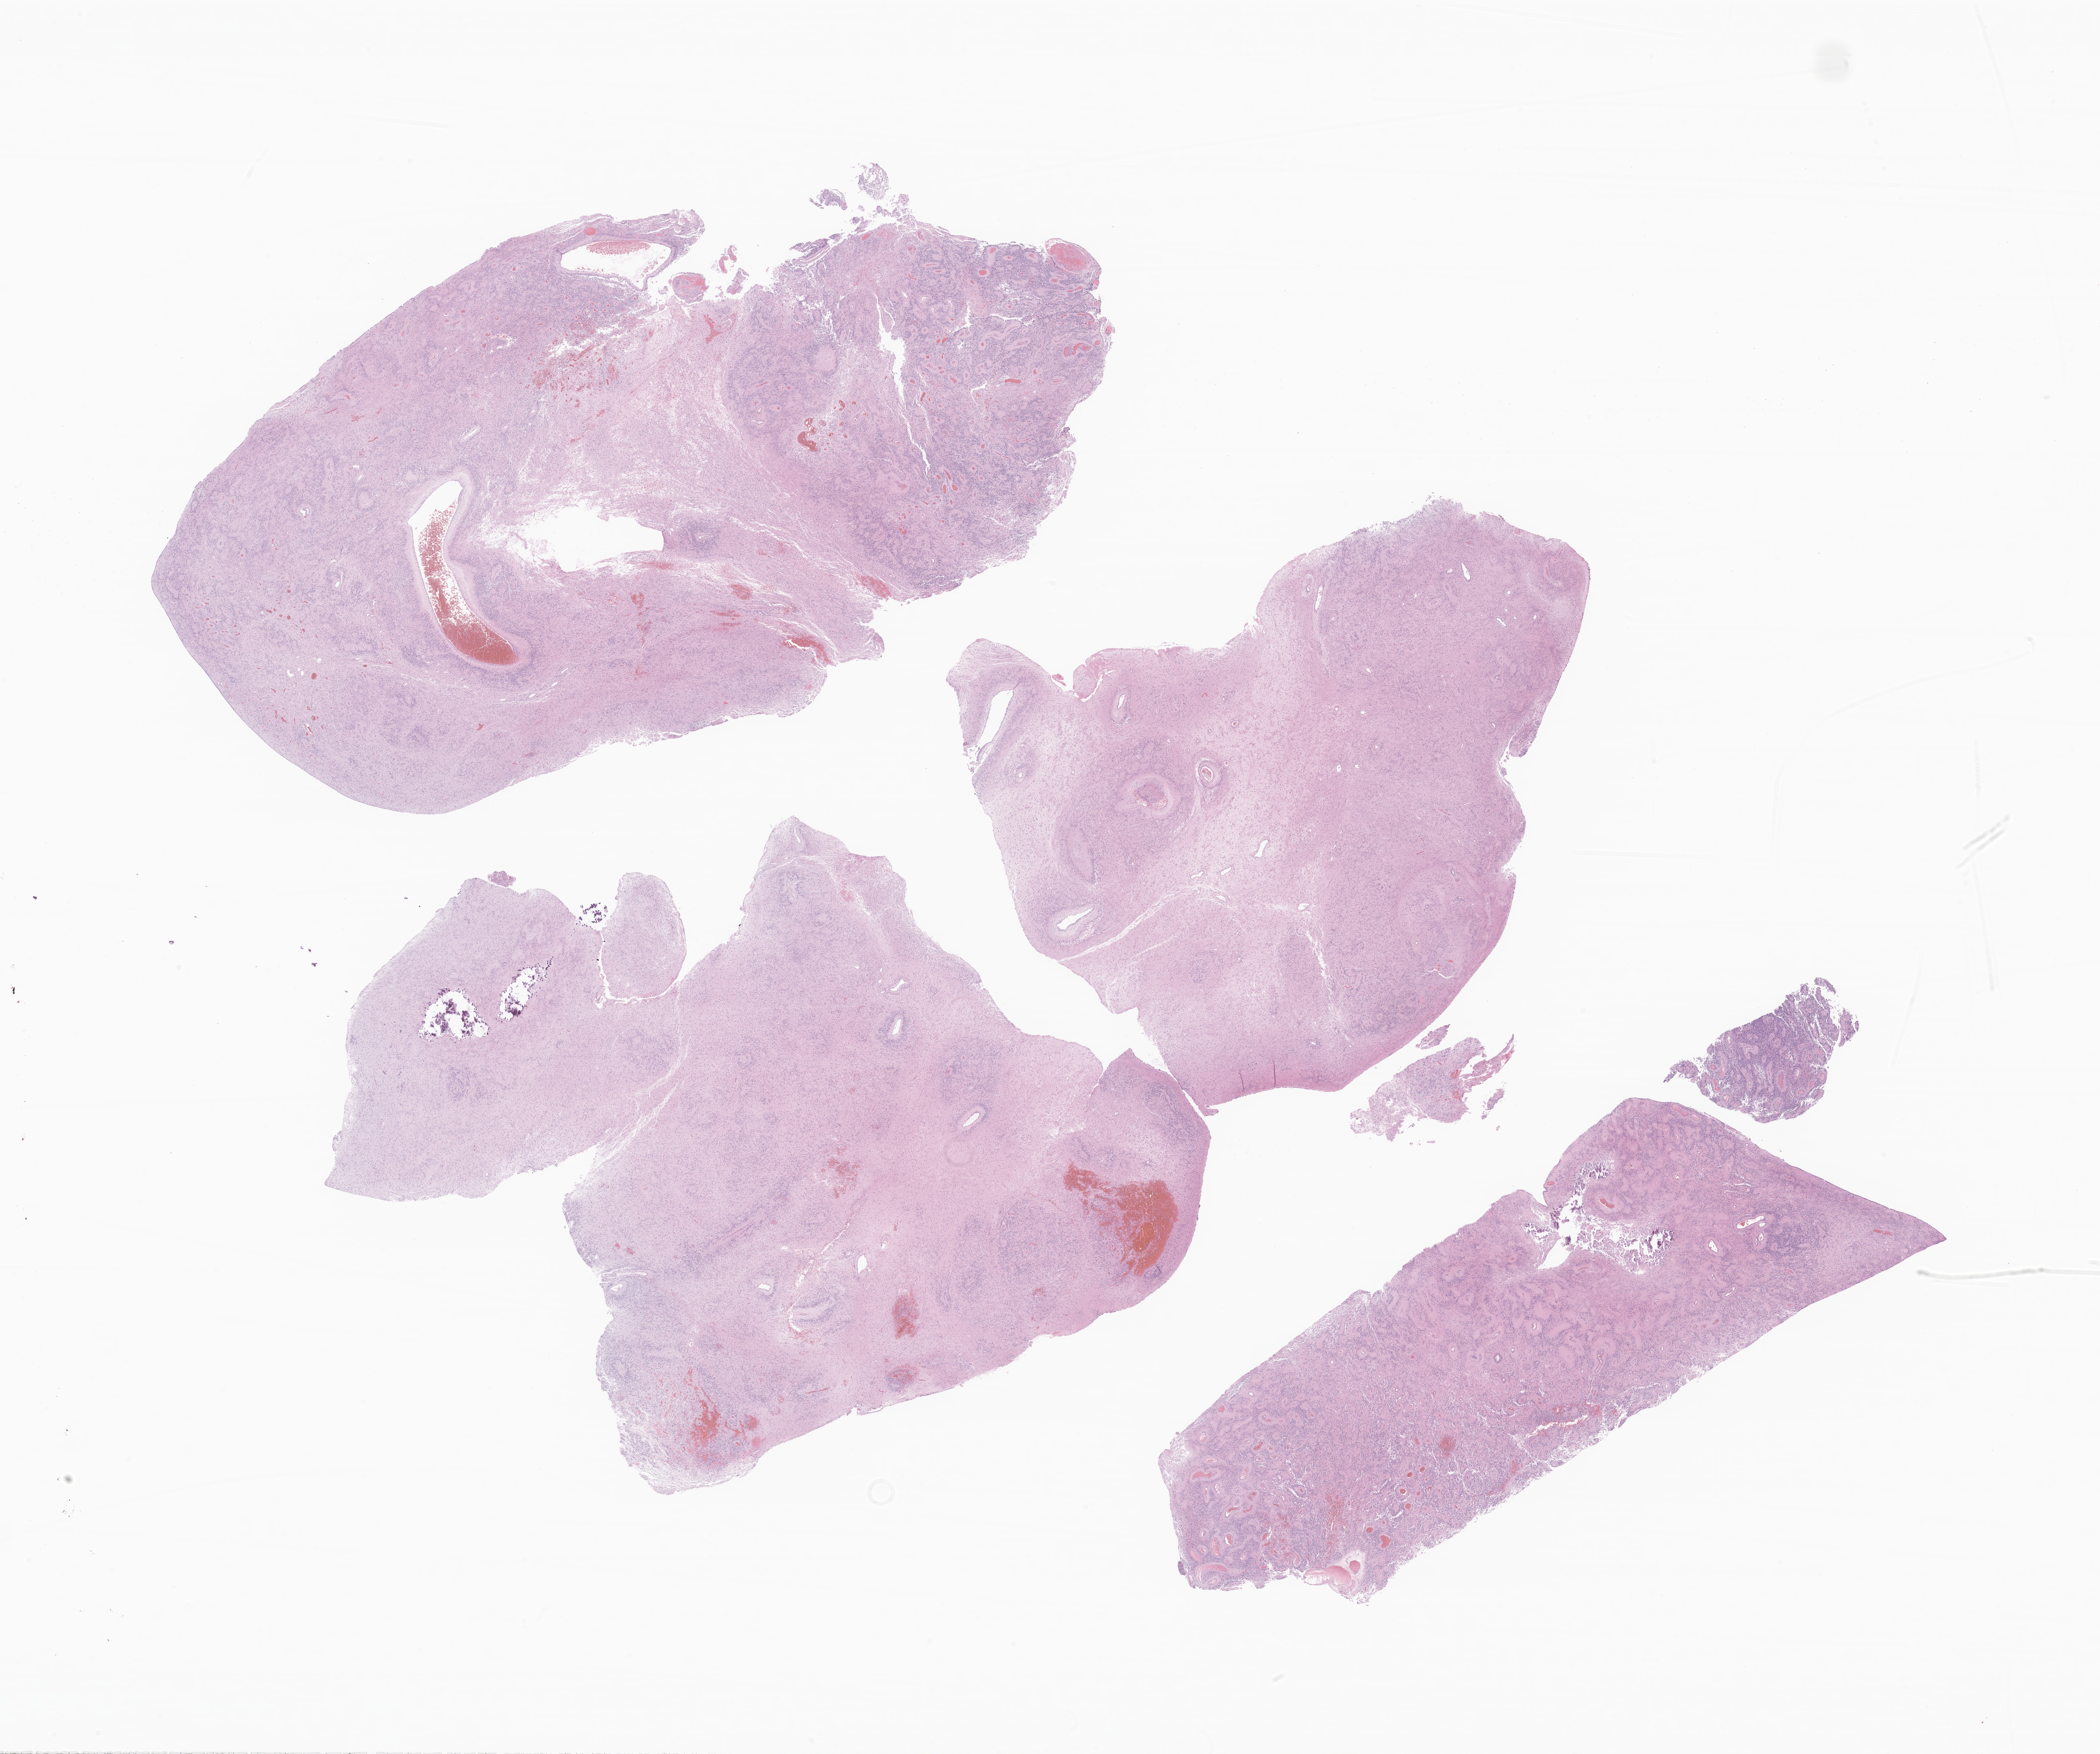
Haematoxylin and eosin whole-slide image of tumor tissue from the brain — a low-resolution overview of the entire scanned area, about 26.3 x 22.0 mm, FFPE section. Patient: male, age 44 months (3 years 8 months).
Diagnosis: Ependymoma, NOS.